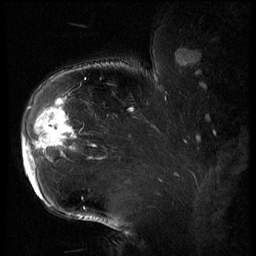
Breast MRI (dynamic contrast-enhanced), one sagittal slice; 3 images stored at this slice position (order not interpretable as contrast timing); 1.5 T; TE 4.2 ms, TR 9 ms; 2.5 mm slice thickness; 256 × 256 image matrix. Patient: female, 43 years. From the clinical record (not read from this slice): setting: breast cancer imaged before/during neoadjuvant chemotherapy; receptor status: HER2-positive.
Annotated regions visible in this slice (semi-automatically segmented with operator editing):
- analysis volume of interest (the breast-tissue region the enhancement analysis was run in; not a lesion): box from (x=22, y=90) to (x=82, y=203) px
- tumour enhancement mask (voxels above the 140 % enhancement threshold inside the analysis volume of interest): (x=23, y=98)–(x=79, y=195)